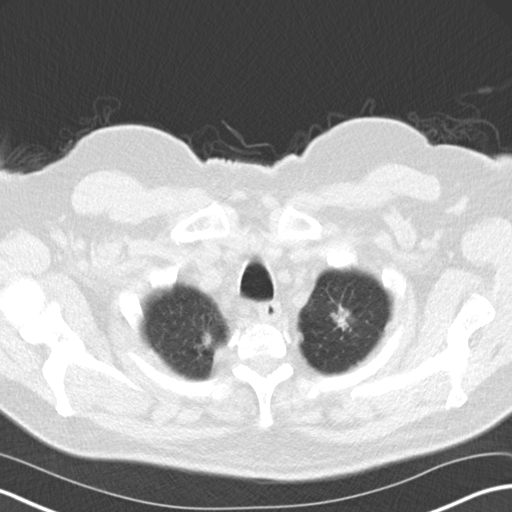
Axial slice from a low-dose chest CT screening exam, third annual screen, lung window (W 1500 / L -600 HU), 5 mm slice thickness, 120 kVp. Male participant, aged 67 years at enrolment. Former smoker at enrolment.
Expert-annotated lung lesion, bounding box (x1, y1, x2, y2) in pixels: (321, 300, 361, 340). The exam's reader record, not a measurement of the box and not confirmed to be the same lesion: non-calcified nodule or mass ≥4 mm, left upper lobe, 20 × 15 mm, spiculated (stellate) margins, soft tissue attenuation, pre-existing on the prior screen: yes; interval growth: yes.